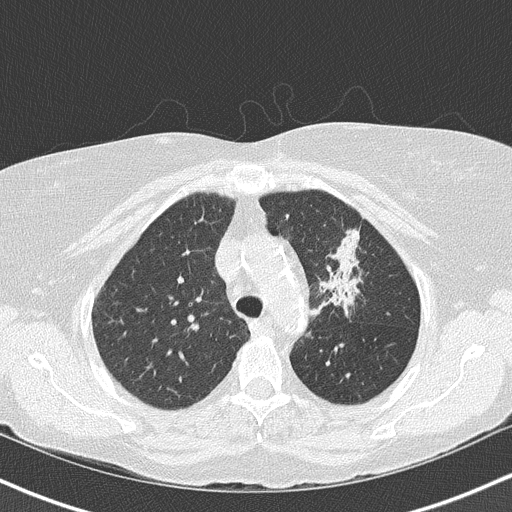
Low-dose screening chest CT, one axial slice. Slice 113 of 147 in the series (ordered by position). Reconstruction kernel B50f. Lung window (W 1500 / L -600 HU). 2 mm slice thickness. 512 × 512 image matrix.
Outlined on this slice (outlined manually by an expert reader):
- lesion 1 (tumor, upper lobe of left lung): box from (x=320, y=229) to (x=359, y=309) px